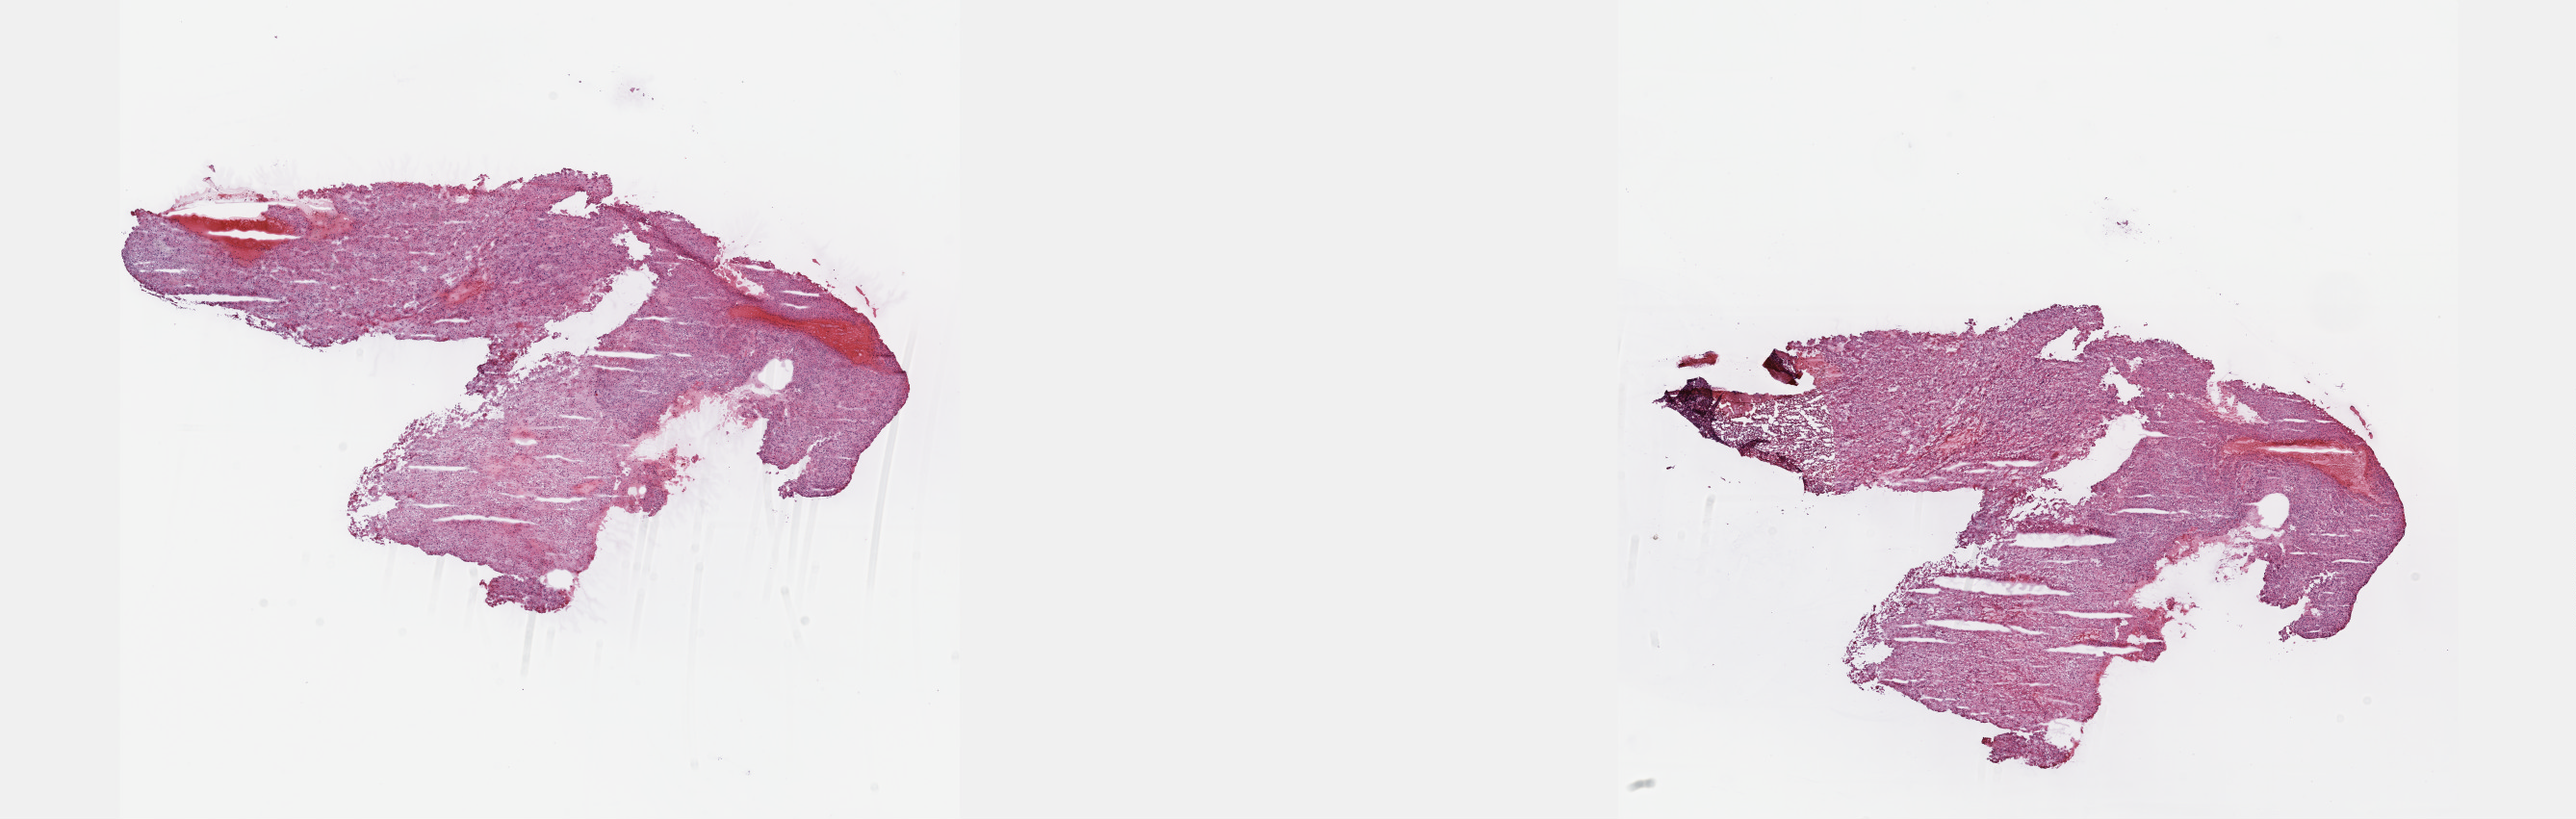
H&E whole-slide image — shown as a low-resolution overview of the whole scanned area (about 21.6 x 6.9 mm). Frozen section from the top of the tissue portion. Sample: primary tumour, liver. Male patient; age at initial diagnosis 66 years. Histologic grade: G2 (moderately differentiated). Slide review estimates, as recorded: tumour cells 87%, tumour nuclei 95%, normal cells 0%, stromal cells 10%, necrosis 3%. Inflammatory infiltration, as recorded: lymphocyte infiltration 3%, monocyte infiltration 1%, neutrophil infiltration 0%.
• diagnosis: Hepatocellular carcinoma, NOS
• AJCC pathologic stage: I